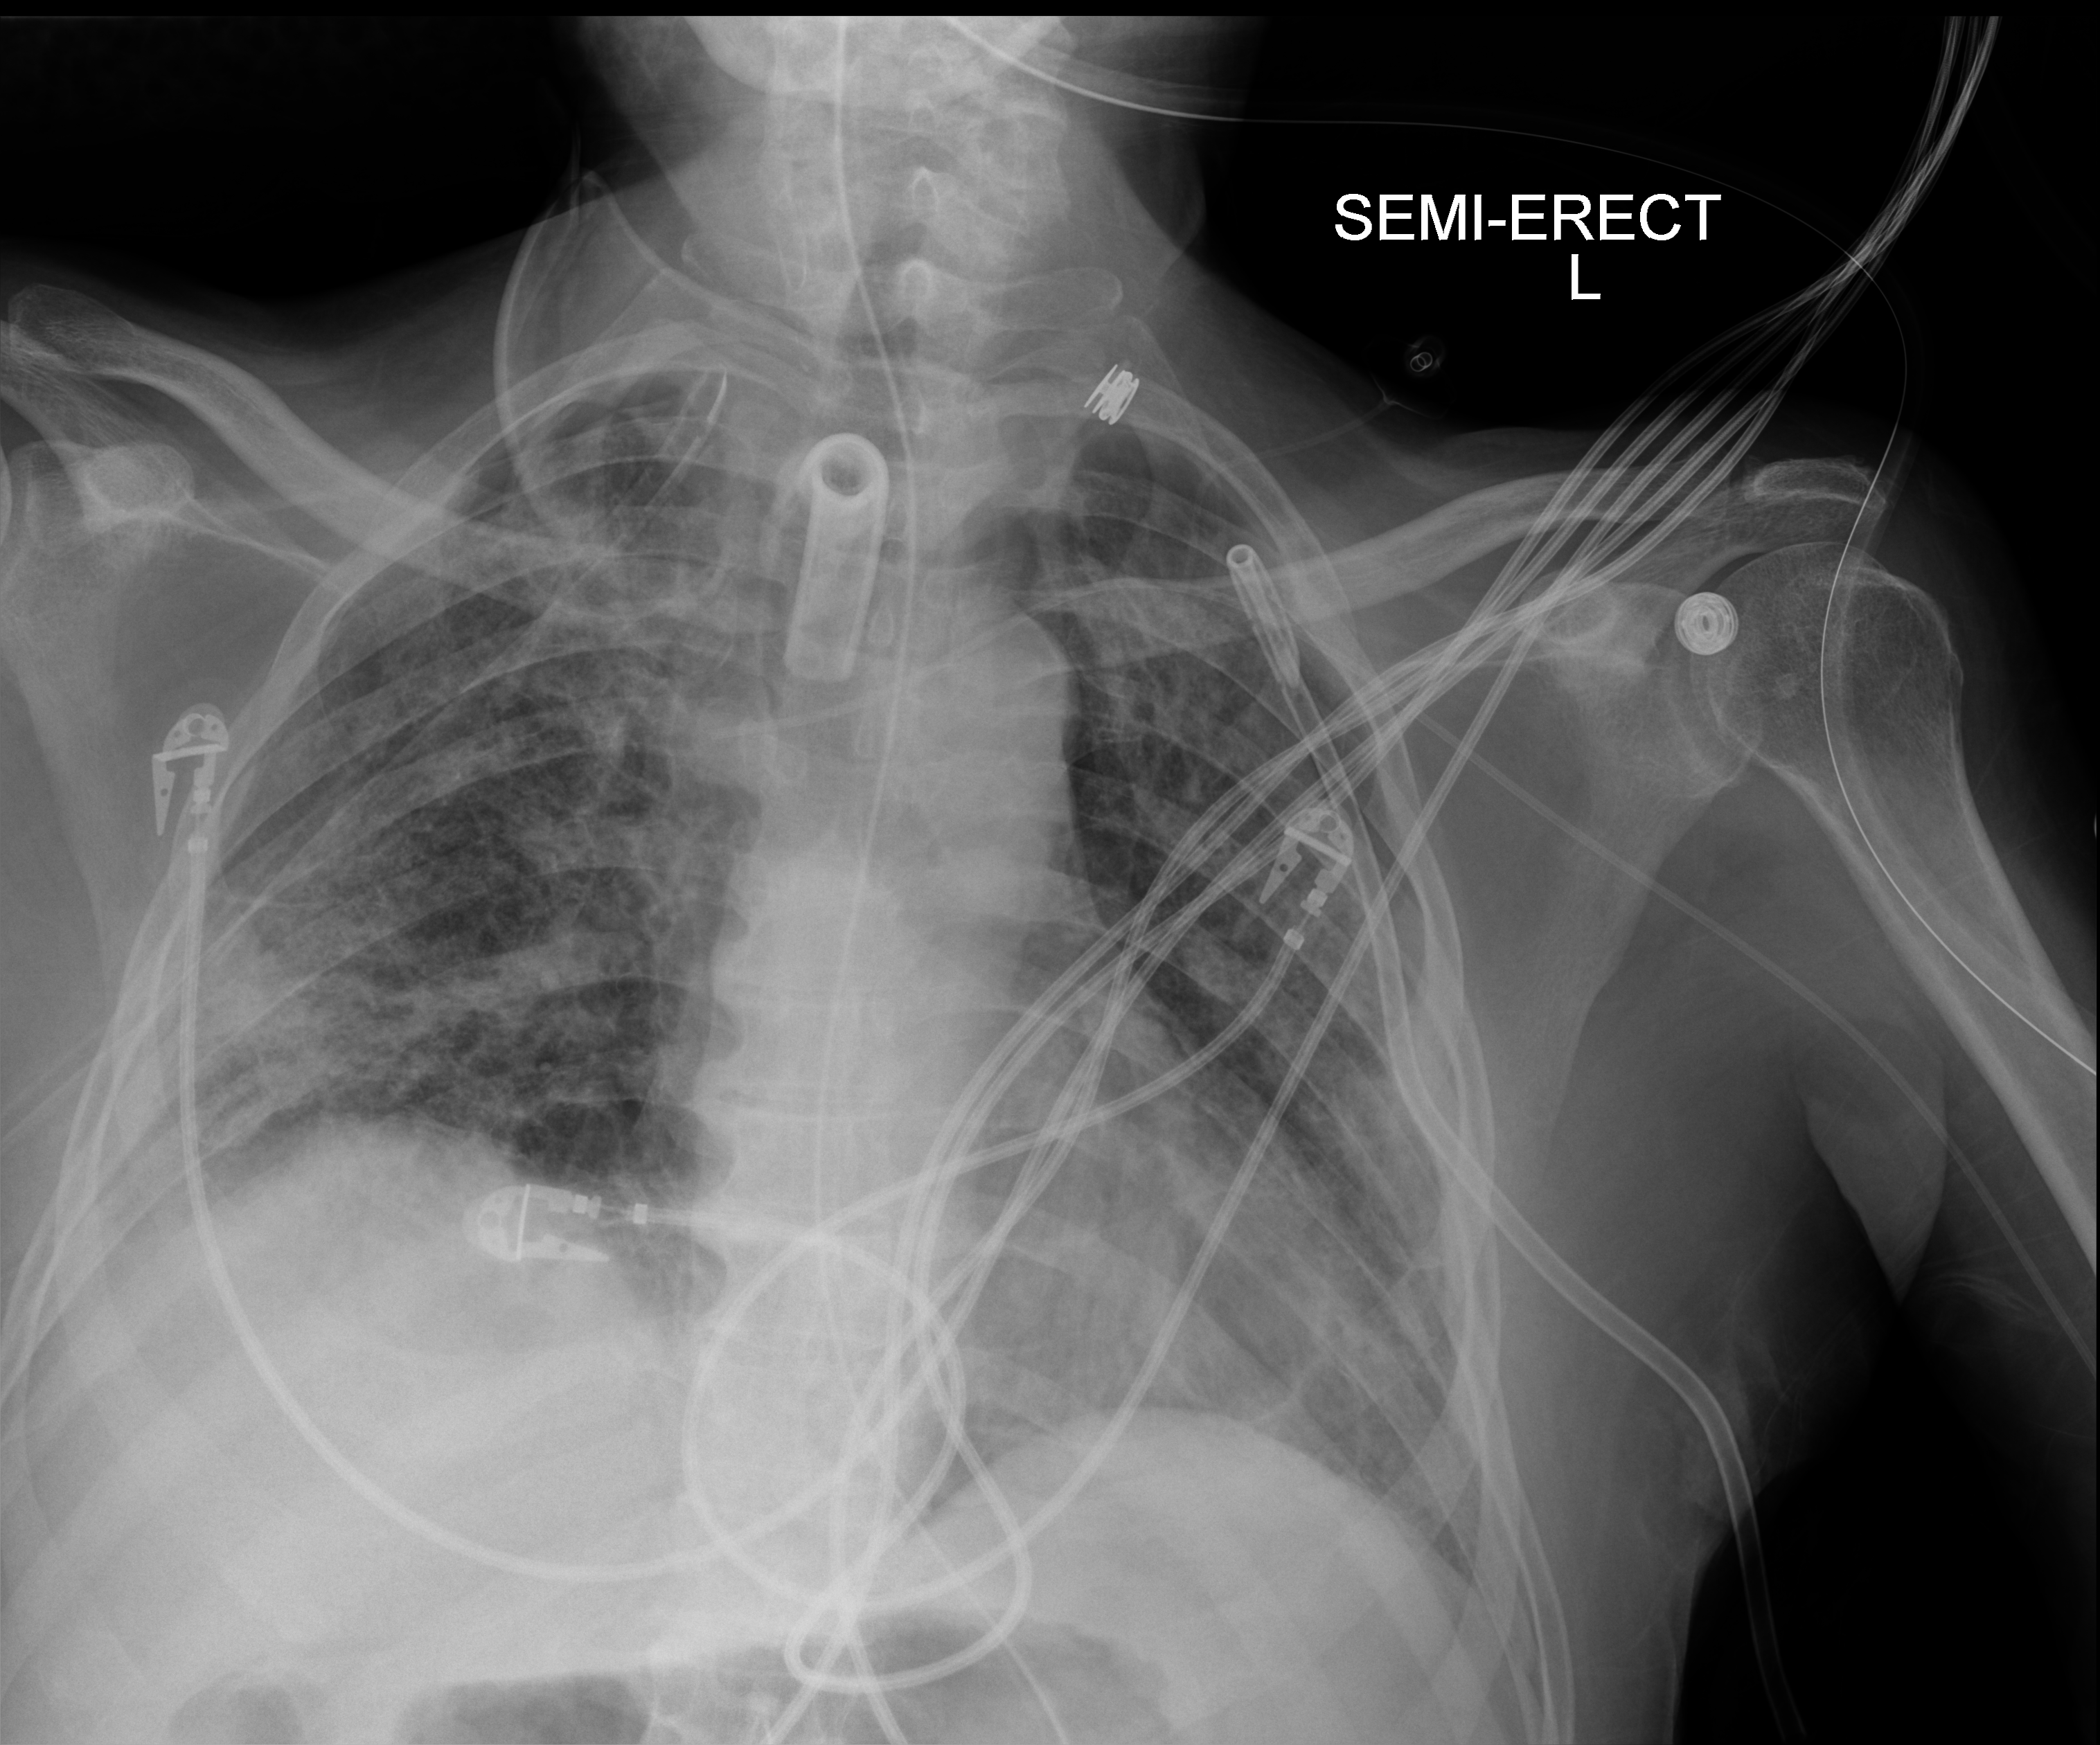
Portable chest radiograph, anteroposterior (AP) projection. Patient hospitalised with COVID-19; male, aged 18–59 years.
Hospital-stay facts (about this admission, not read from this image; timing relative to this image not recorded): admitted to intensive care during this hospital stay: yes; hypertension (admission record): yes; mechanically ventilated during this hospital stay: yes.